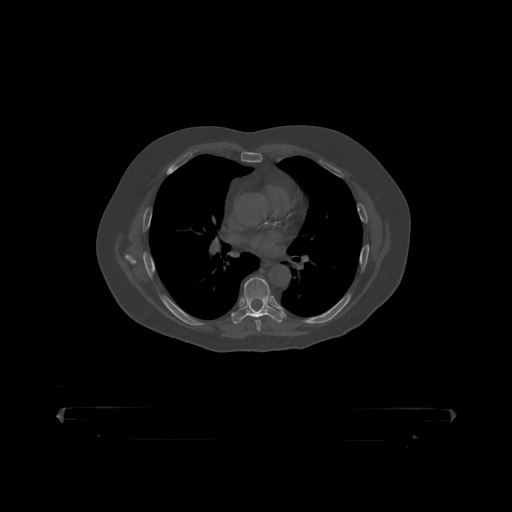
CT including the spine, one axial slice. Reconstruction kernel STANDARD. 120 kVp. Bone window (W 1800 / L 400 HU). 1.25 mm slice thickness. 512 × 512 image matrix. Patient: male, 60 years. Case-level facts recorded for this patient, not image findings: primary cancer: prostate.
Outlined on this slice (semi-automatically segmented with operator editing):
- T7 vertebra: bounding box <233,277,280,319> (left, top, right, bottom; pixels)